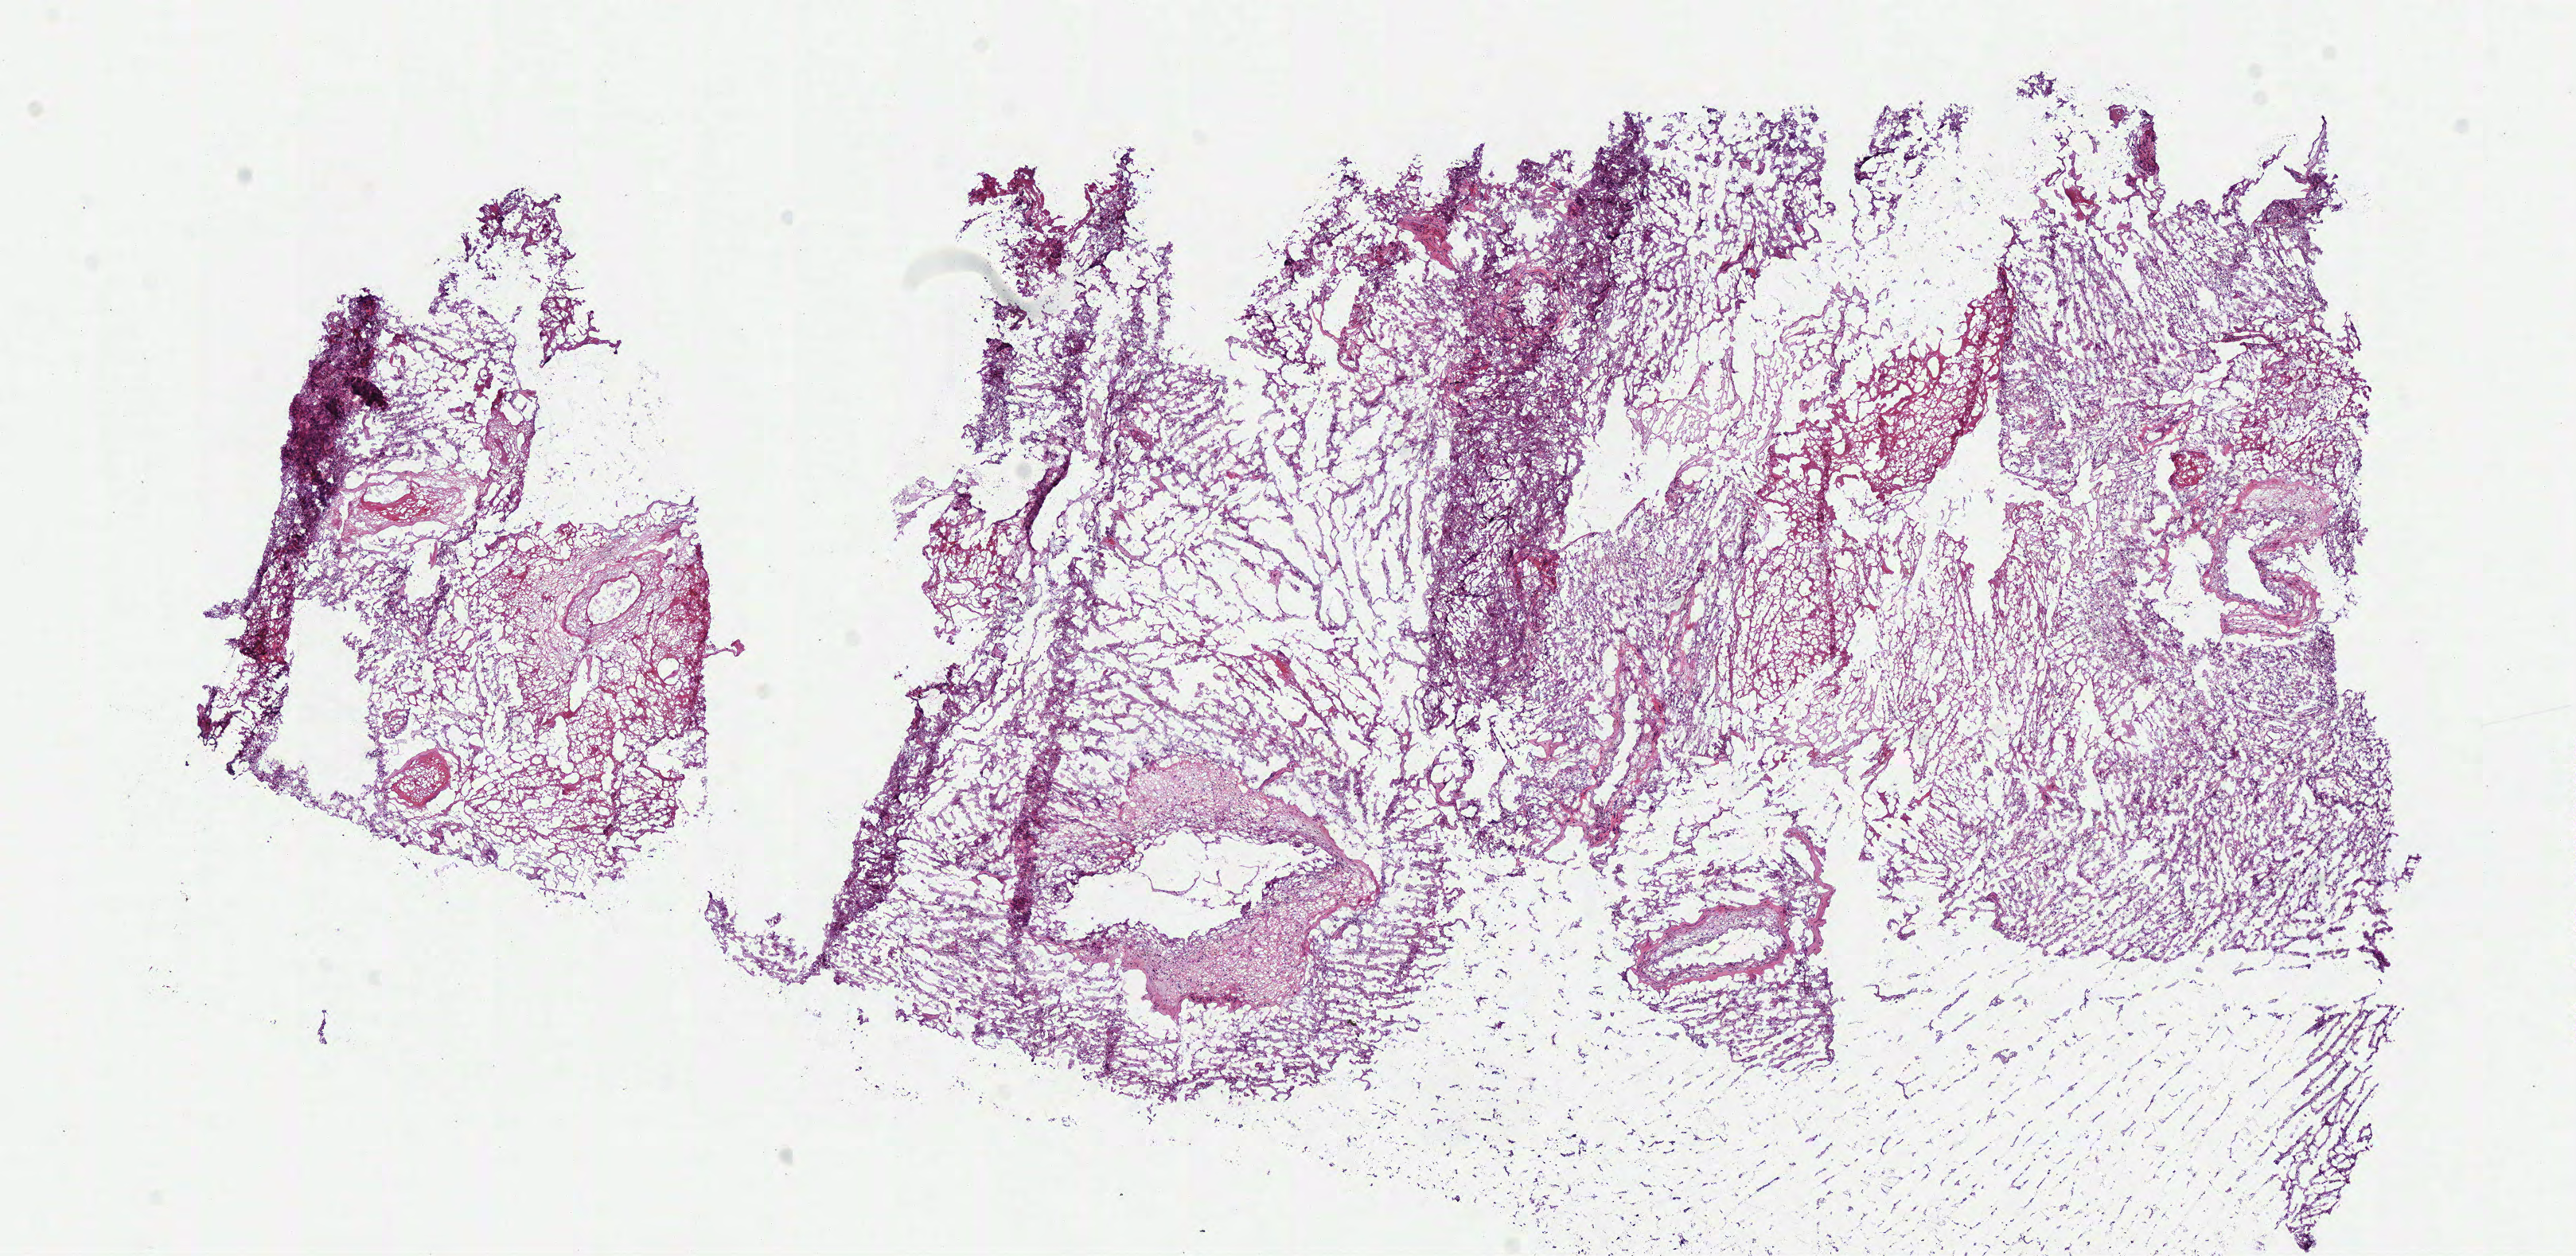
H&E whole-slide image, a low-resolution overview of the entire scanned area, about 12.7 x 6.2 mm (from a 40x scan); frozen section from the bottom of the tissue portion; sample: primary tumour, brain. Male patient; age at initial diagnosis 74 years. Composition of this section per pathologist review: tumour cells 87%, tumour nuclei 65%, normal cells 0%, stromal cells 8%, necrosis 5%.
Pathologic diagnosis: Glioblastoma.